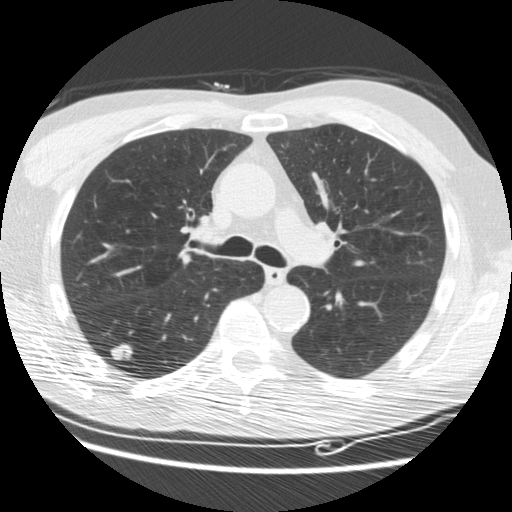
Low-dose screening chest CT, one axial slice; slice 111 of 176 in the series (ordered by position); 120 kVp; lung window (W 1500 / L -600 HU); 512 × 512 image matrix, field of view 347 × 347 mm.
Annotated regions visible in this slice (expert manual segmentation):
- lesion 1 (tumor, lower lobe of right lung): bounding box (x1, y1, x2, y2) in pixels: (110, 344, 133, 361)